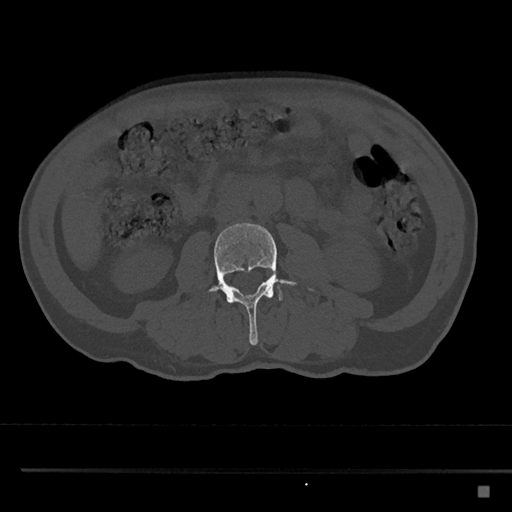
CT including the spine, one axial slice. Position 692 of 797 along the scan axis. Reconstruction kernel Br40s/3. Bone window (W 1800 / L 400 HU). 0.5 mm slice thickness. 512 × 512 image matrix, field of view 391 × 391 mm. Patient: male, 59 years. Case-level facts recorded for this patient, not image findings: primary cancer: prostate.
Outlined on this slice (semi-automatically segmented with operator editing):
- L3 vertebra: bounding box <210,223,311,345> (left, top, right, bottom; pixels)
- L4 vertebra: <279,291,283,301>